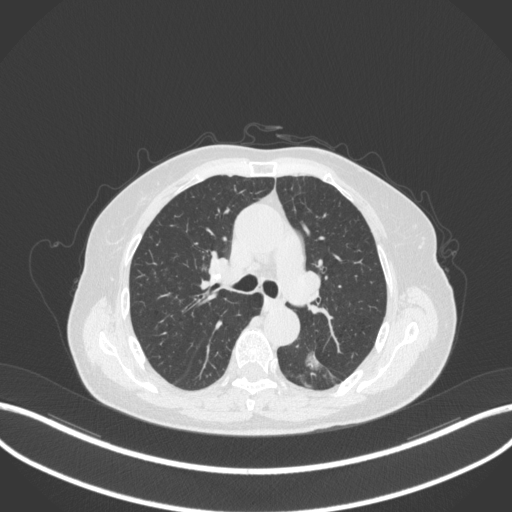
Chest CT, one axial slice. Lung window (W 1500 / L -600 HU). 512 × 512 image matrix. Patient: female, 70 years. From the clinical record (not read from this slice): clinical TNM (as recorded): T1c N0 M0.
Structures marked on this image (rectangle marked by the reading radiologist):
- lung tumour (recorded histology: adenocarcinoma): bounding box [x1, y1, x2, y2] px = [305, 347, 324, 372]